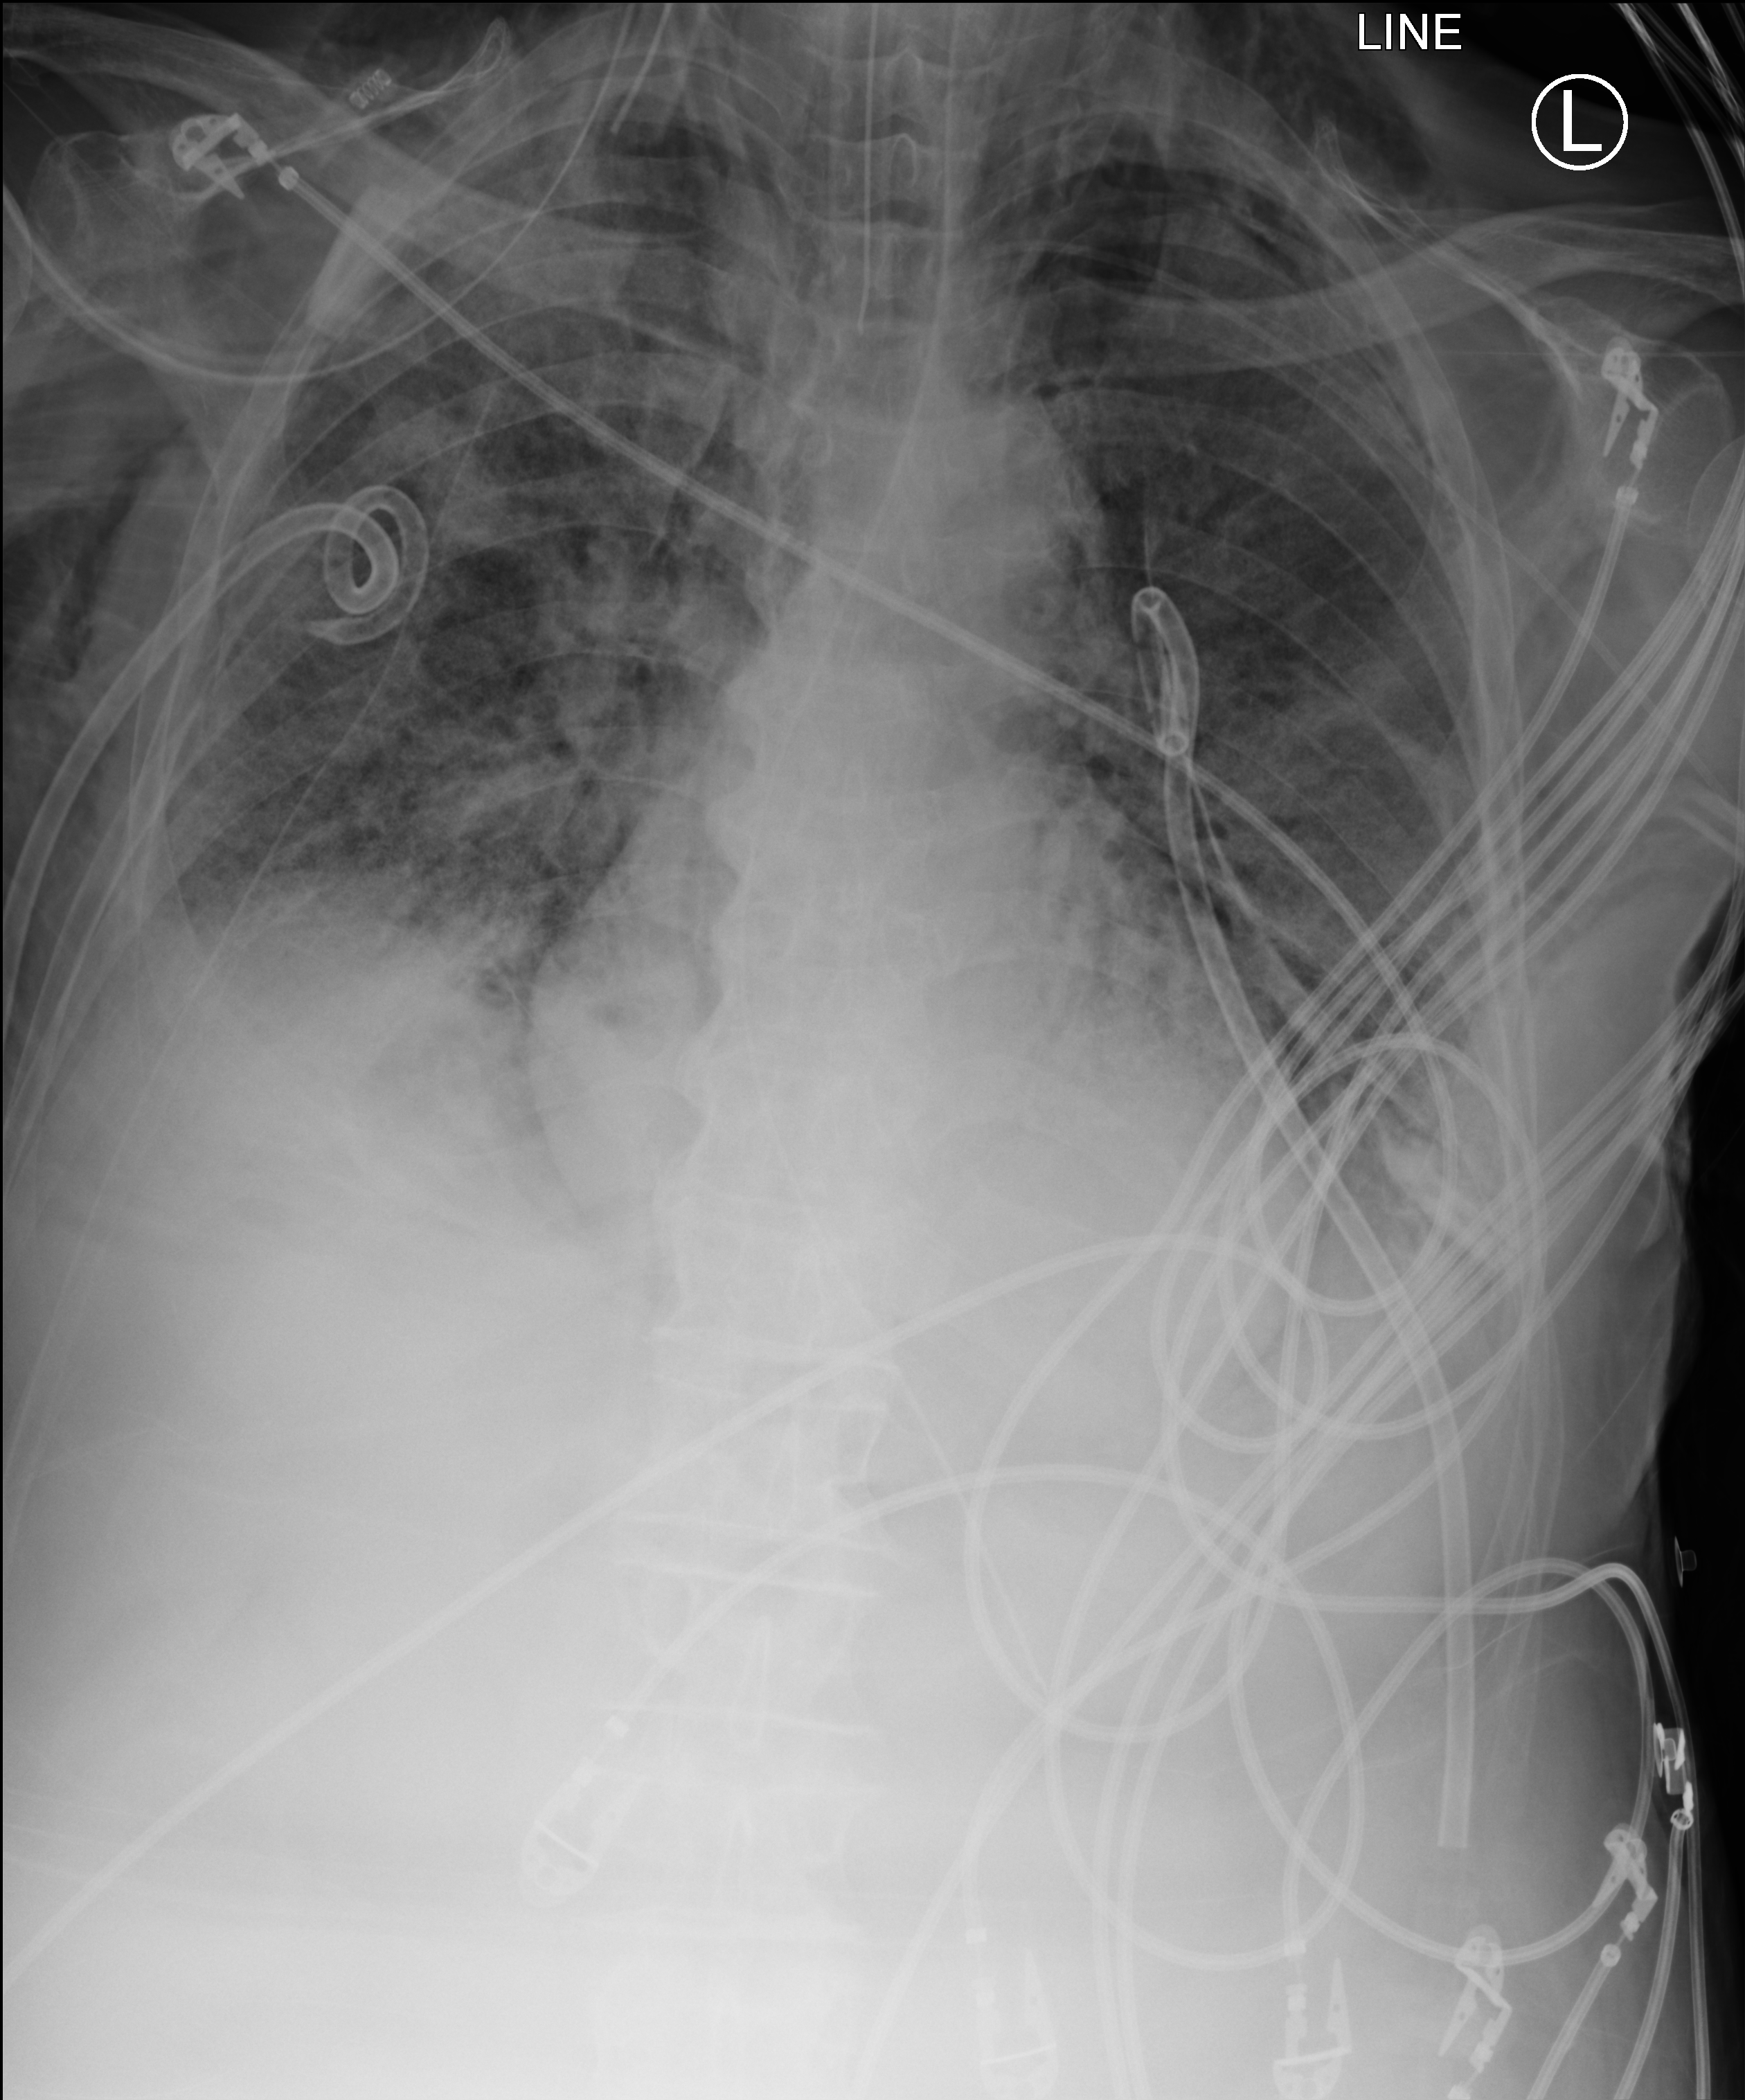
Portable chest radiograph. Patient hospitalised with COVID-19; male, aged 75–90 years.
Hospital-stay facts (about this admission, not read from this image; timing relative to this image not recorded): hypertension (admission record): yes; smoking status (admission record): never.